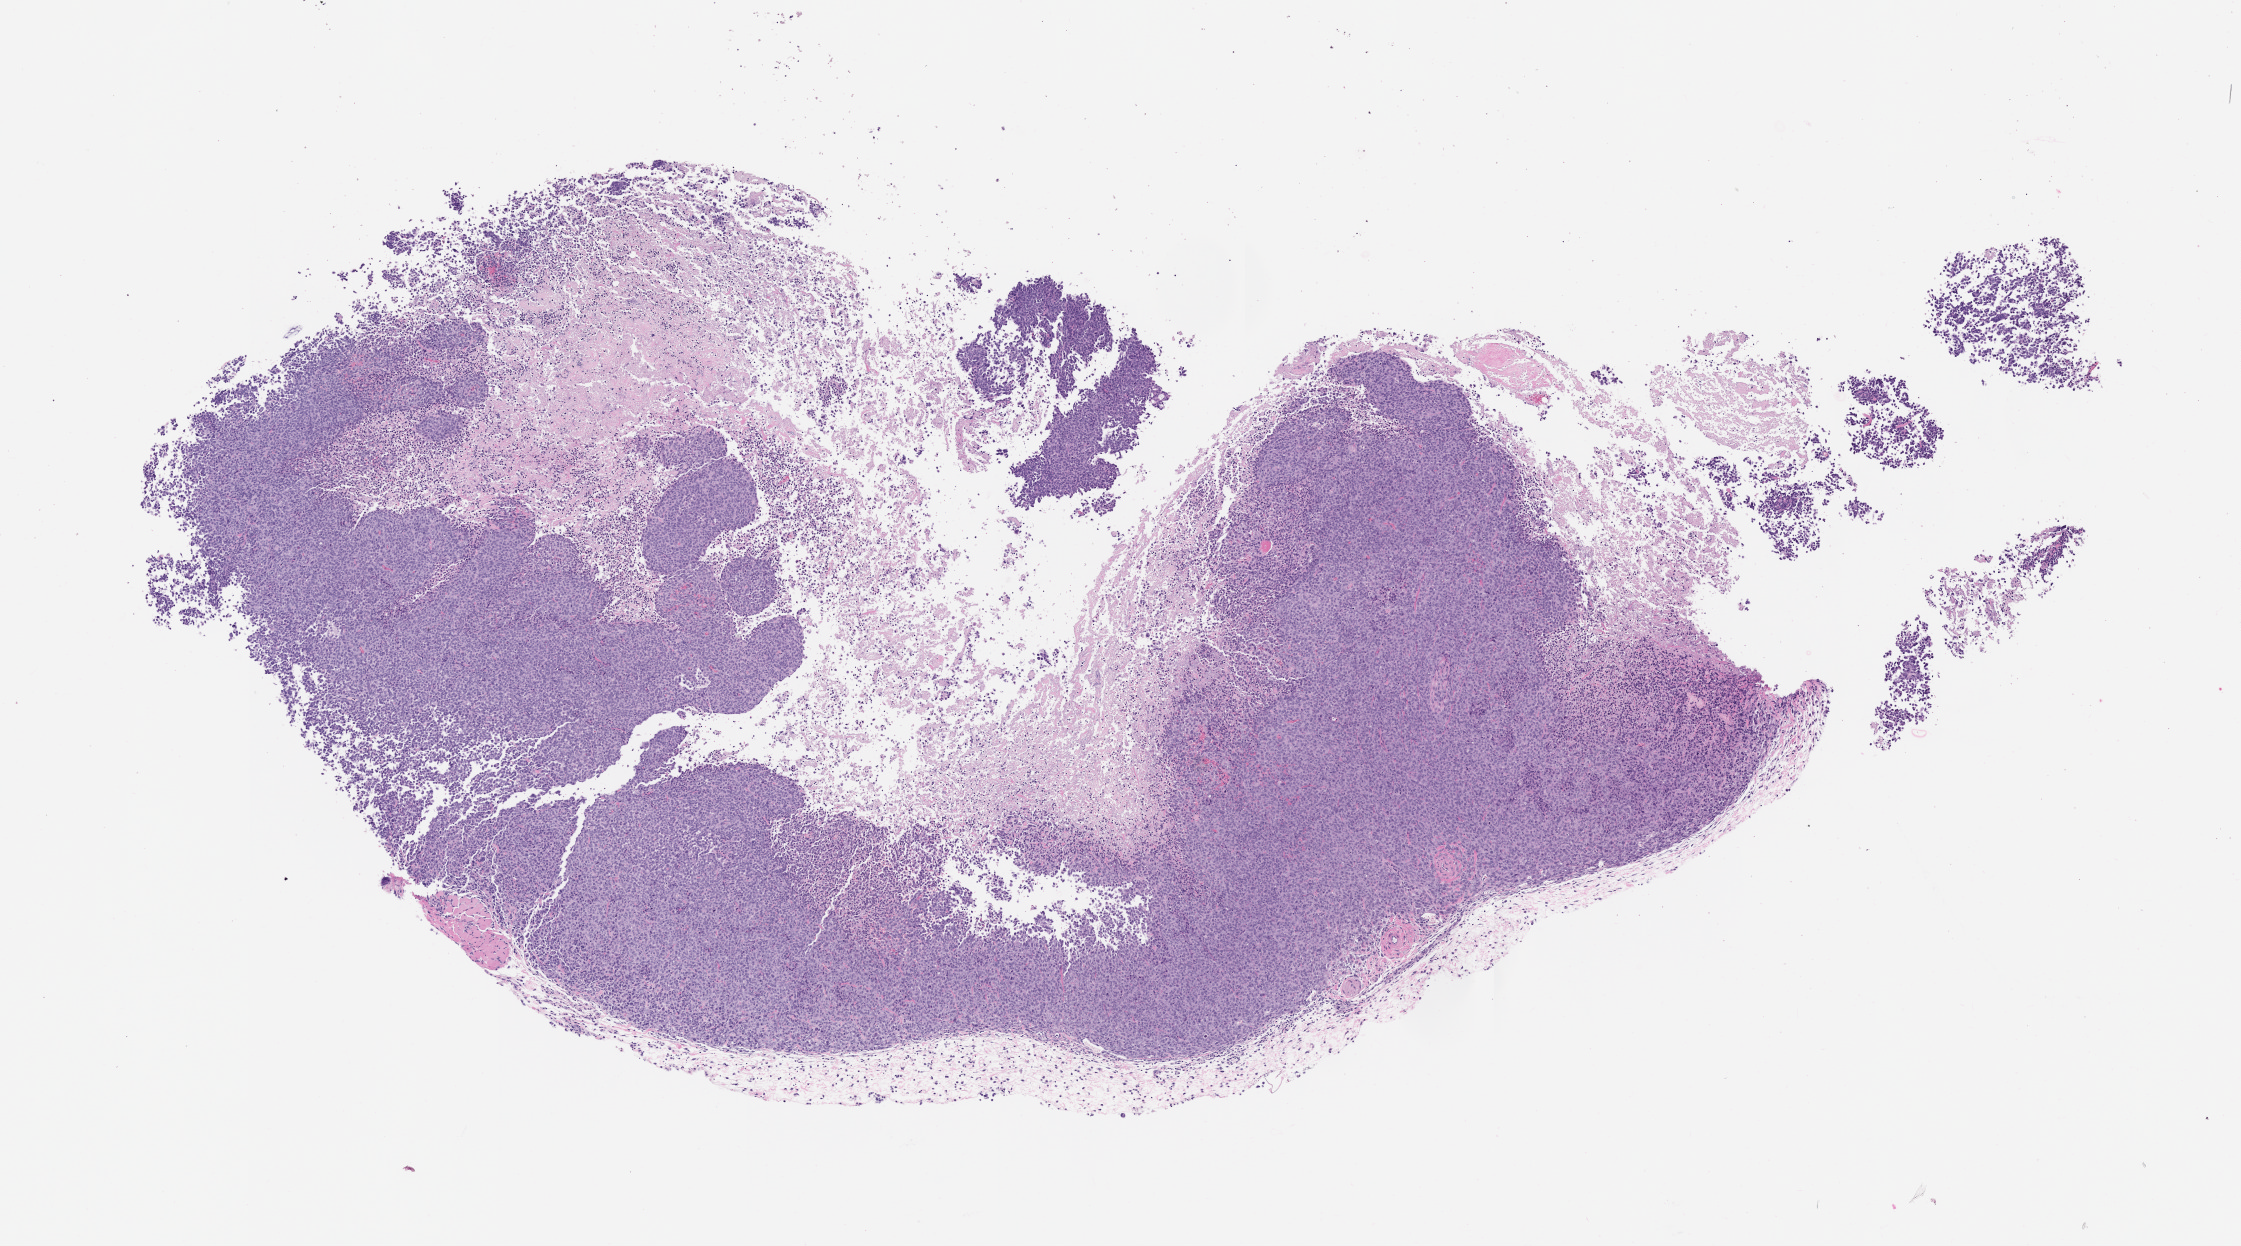
Whole-slide image, haematoxylin and eosin: patient-derived xenograft (human tumor grown in a mouse), passage 2, shown as a low-resolution overview of the whole scanned area (about 9.0 x 5.0 mm), formalin-fixed paraffin-embedded section, tumor site category: pancreas.
* originating patient diagnosis: Pancreatic Adenocarcinoma